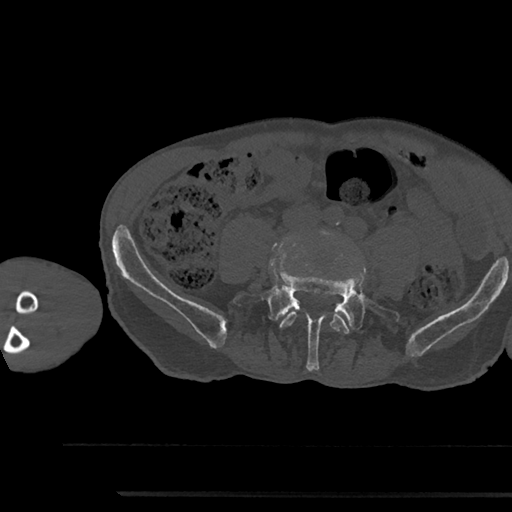
CT including the spine, one axial slice; position 369 of 797 along the scan axis; bone window (W 1800 / L 400 HU); 512 × 512 image matrix, field of view 367 × 367 mm. Male patient, age 79 years. From the clinical record (not read from this slice): primary cancer: prostate.
Annotated regions visible in this slice (semi-automatically segmented with operator editing):
- L4 vertebra: bounding box <280,310,349,334> (left, top, right, bottom; pixels)
- L5 vertebra: <233,264,400,370>